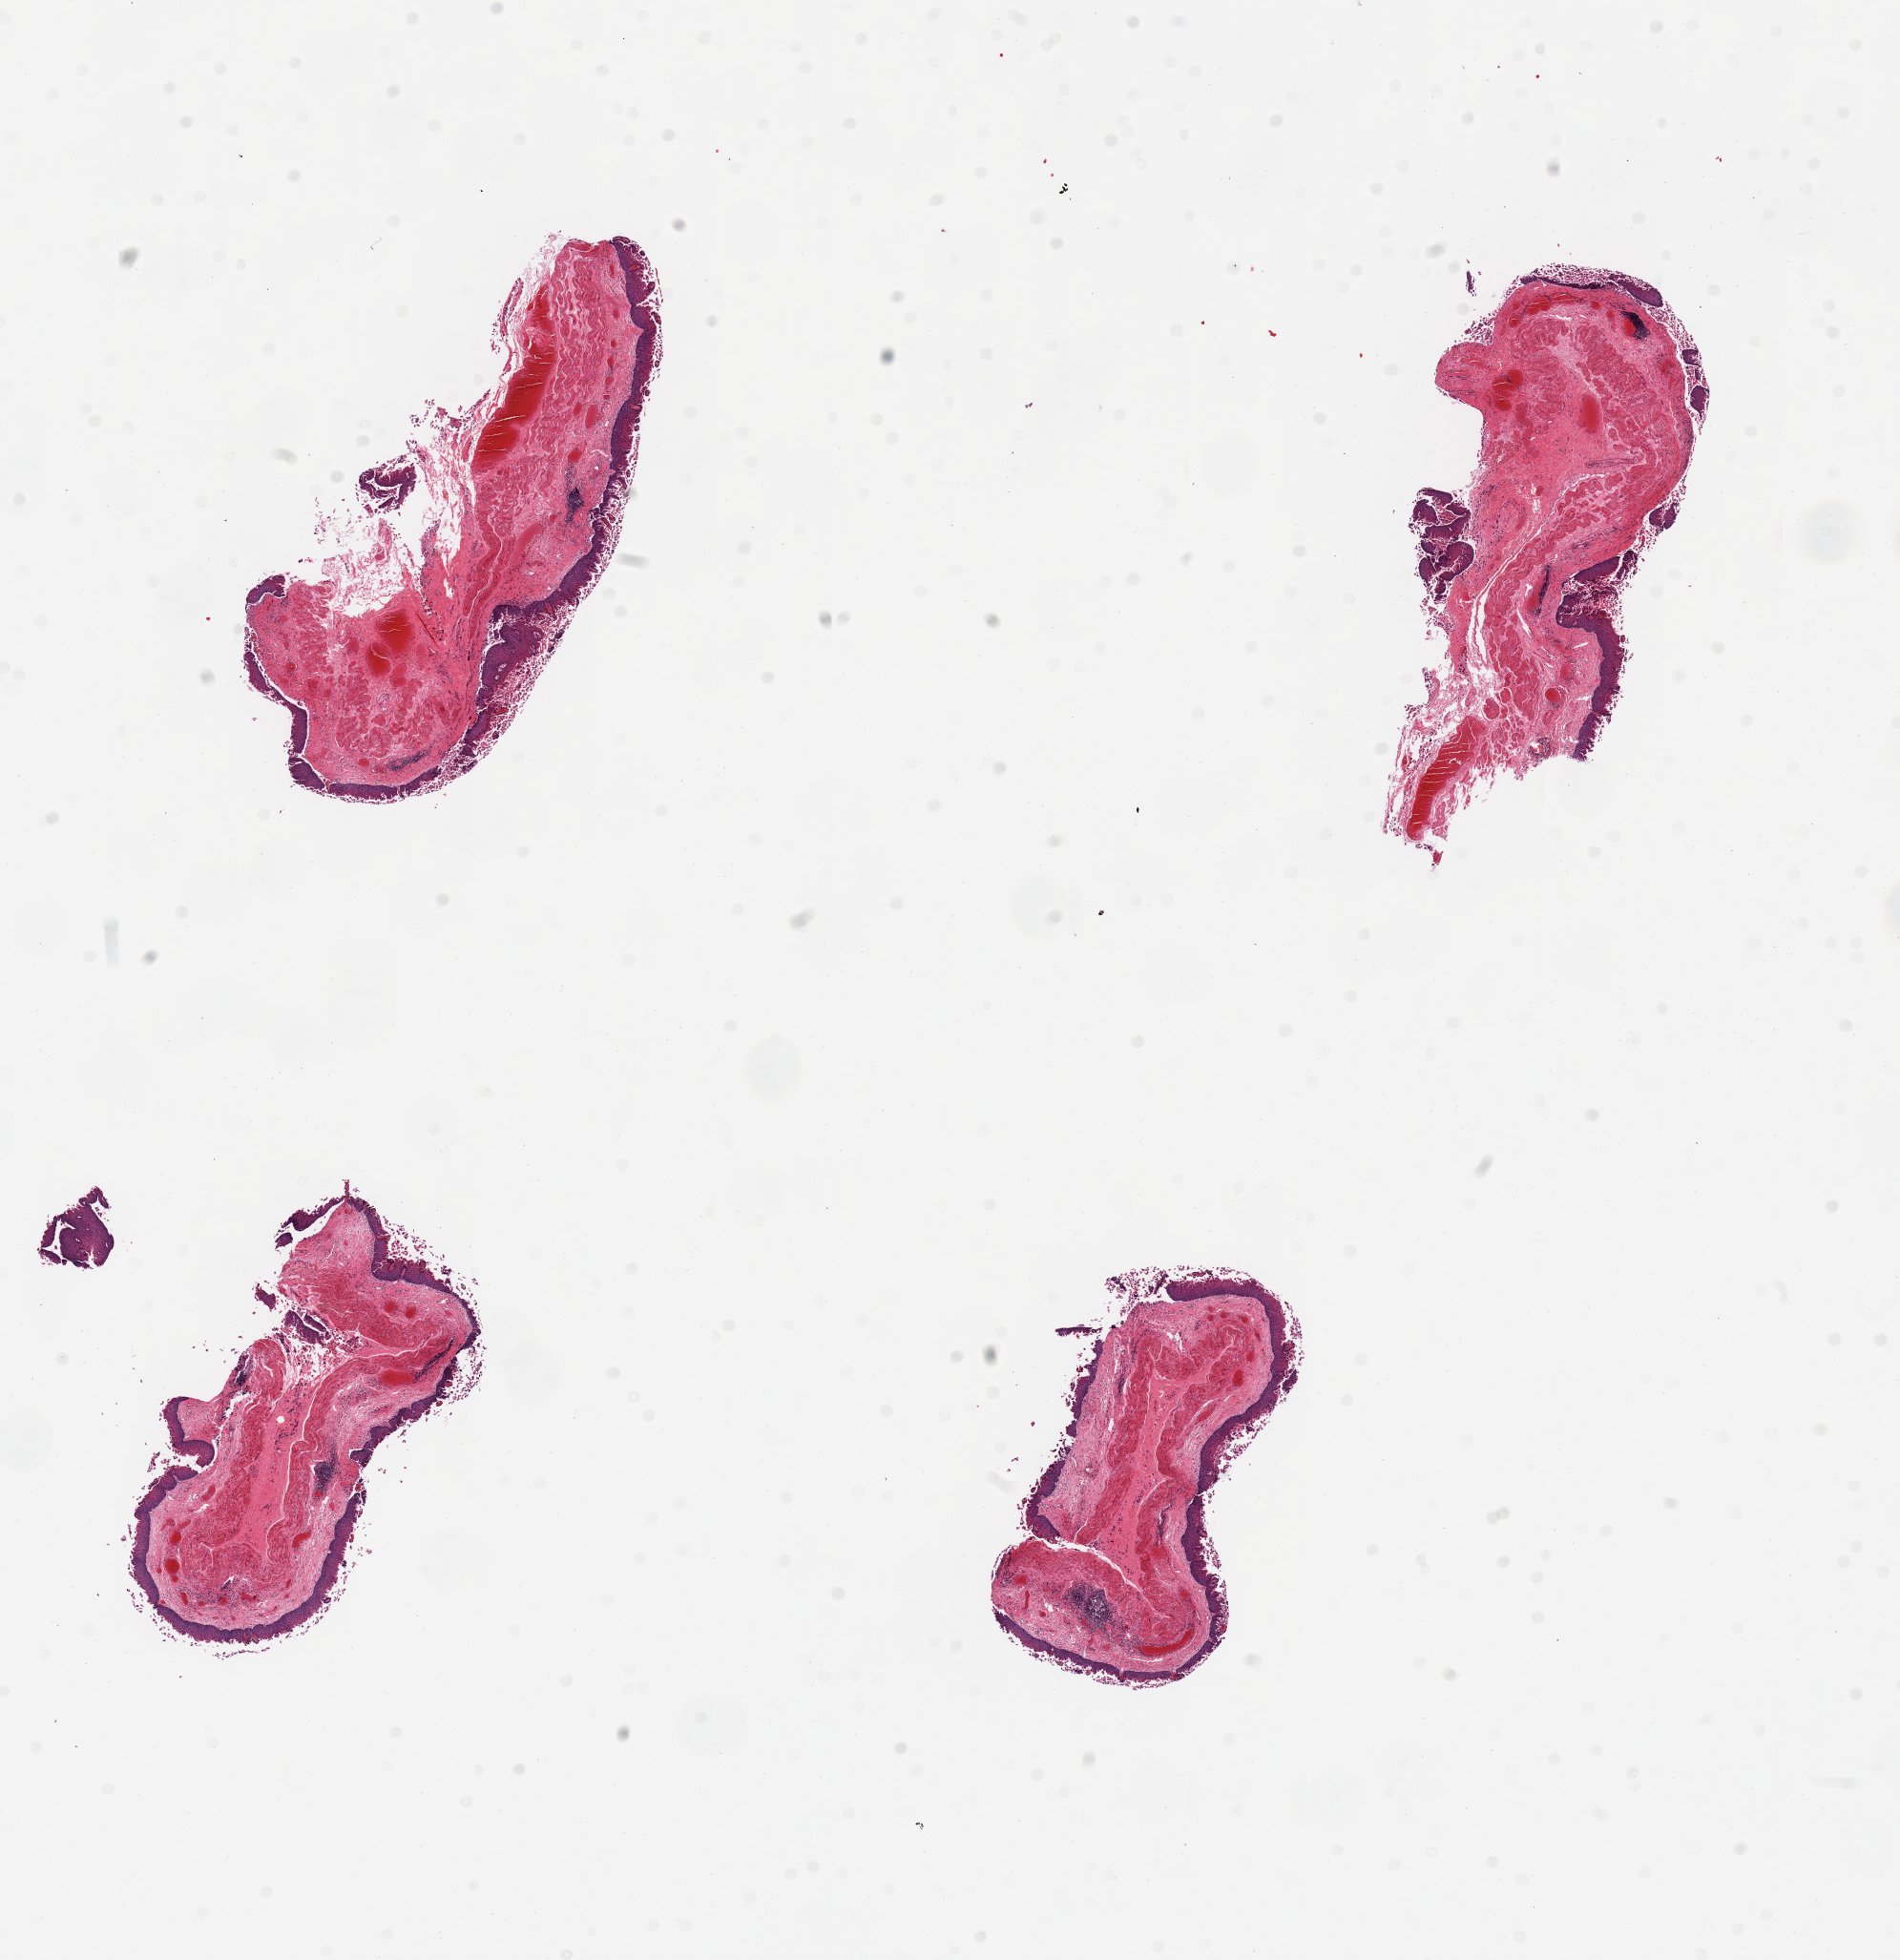
Digitized hematoxylin and eosin (H&E)-stained section, low-resolution overview of the scanned area, about 15.8 x 16.2 mm (acquisition: 20x scan). PAXgene-fixed, paraffin-embedded tissue. Section of esophageal mucous membrane (target tissue). Donor tissue sample. Donor sex: male.
Reviewer comment on this tissue sample: 4 pieces, epithelium partially sloughed, congested.